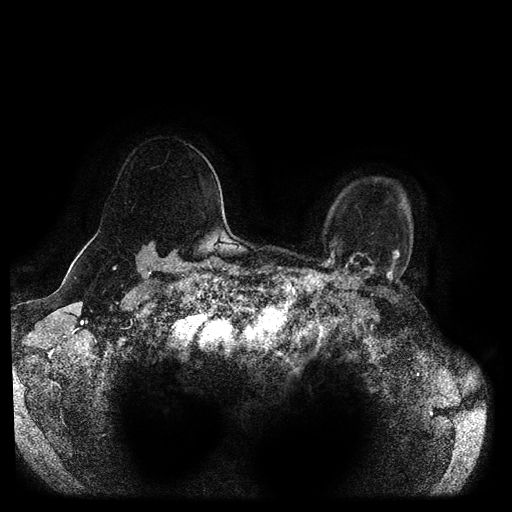
Breast MRI (dynamic contrast-enhanced, multi-phase), one axial slice; position 84 of 116 along the scan axis; dynamic contrast-enhanced series, time point 2 of 5 at this slice position (early post-contrast); 1.5 T; TE 2.6 ms, TR 5.3 ms; 2 mm slice thickness; 512 × 512 image matrix, field of view 370 × 370 mm. Patient: female, 55 years.
Outlined on this slice (semi-automatically segmented with operator editing):
- breast lesion (labelled benign in the annotation): bounding box [x1, y1, x2, y2] px = [338, 249, 400, 282]